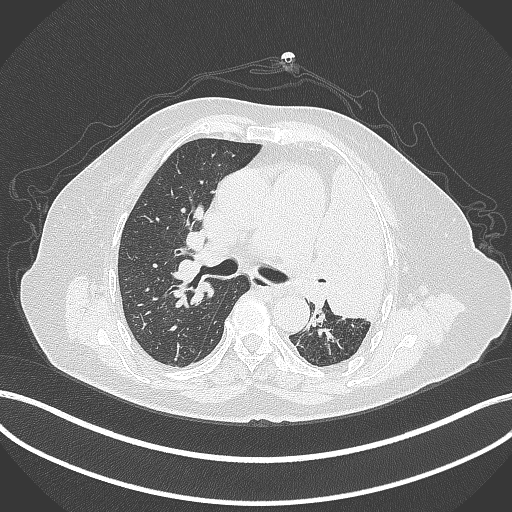
Chest CT, one axial slice; position 240 of 399 along the scan axis; lung window (W 1500 / L -600 HU); 512 × 512 image matrix, field of view 400 × 400 mm. Female patient, age 75 years. From the clinical record (not read from this slice): clinical TNM (as recorded): T3 N3 M1.
Annotated regions visible in this slice (bounding box drawn by a radiologist):
- lung tumour (recorded histology: adenocarcinoma): box from (x=306, y=149) to (x=390, y=324) px